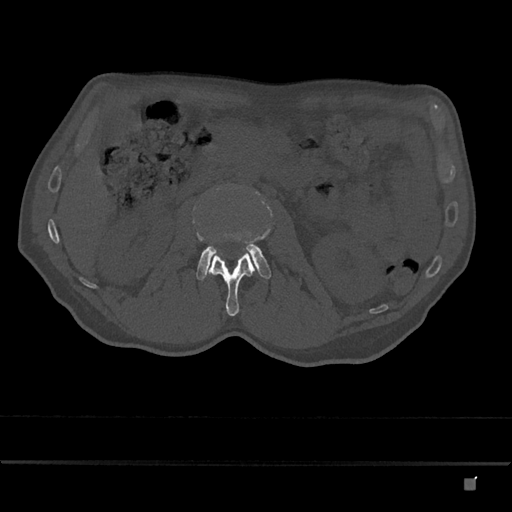
CT including the spine, one axial slice. Bone window (W 1800 / L 400 HU). 0.5 mm slice thickness. 512 × 512 image matrix, field of view 390 × 390 mm. Male patient, age 72 years. Case-level facts recorded for this patient, not image findings: primary cancer: prostate.
Annotated regions visible in this slice (semi-automatically segmented with operator editing):
- L2 vertebra: bounding box <206,250,255,316> (left, top, right, bottom; pixels)
- L3 vertebra: <196,244,271,280>